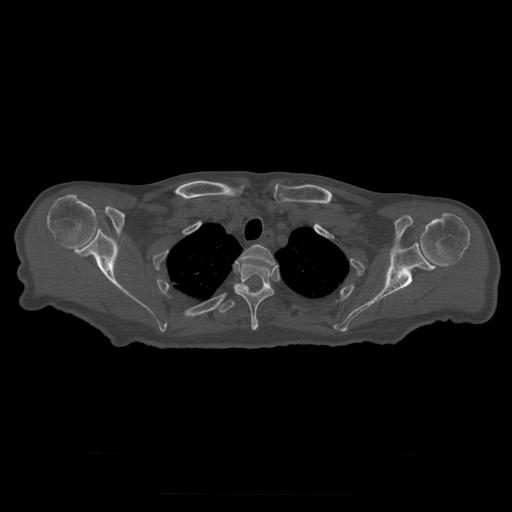
CT including the spine, one axial slice; position 258 of 397 along the scan axis; bone window (W 1800 / L 400 HU); 1.25 mm slice thickness; 512 × 512 image matrix, field of view 510 × 510 mm. Patient age 73 years. From the clinical record (not read from this slice): primary cancer: prostate.
Structures marked on this image (semi-automatic segmentation, software-assisted and operator-edited):
- T2 vertebra: bounding box (x1, y1, x2, y2) in pixels: (239, 244, 277, 266)
- T3 vertebra: (234, 262, 274, 331)
- T4 vertebra: (219, 284, 267, 314)